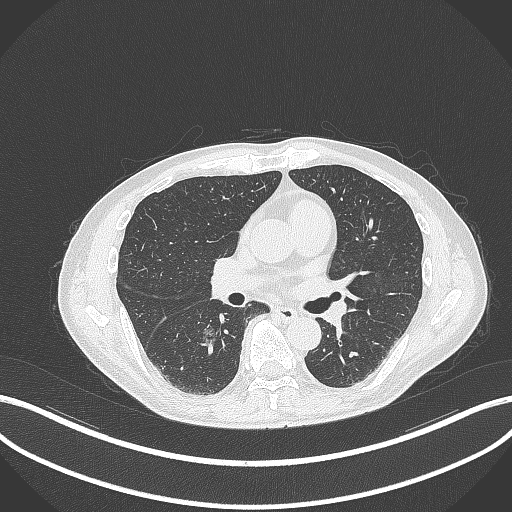
Chest CT, one axial slice. Position 172 of 323 along the scan axis. Reconstruction kernel B70f. 120 kVp. Lung window (W 1500 / L -600 HU). 1 mm slice thickness. 512 × 512 image matrix, field of view 400 × 400 mm. Patient: male, 61 years. From the clinical record (not read from this slice): clinical TNM (as recorded): T1c N0 M0.
Annotated regions visible in this slice (rectangle marked by the reading radiologist):
- lung tumour (recorded histology: adenocarcinoma): box from (x=201, y=320) to (x=221, y=346) px